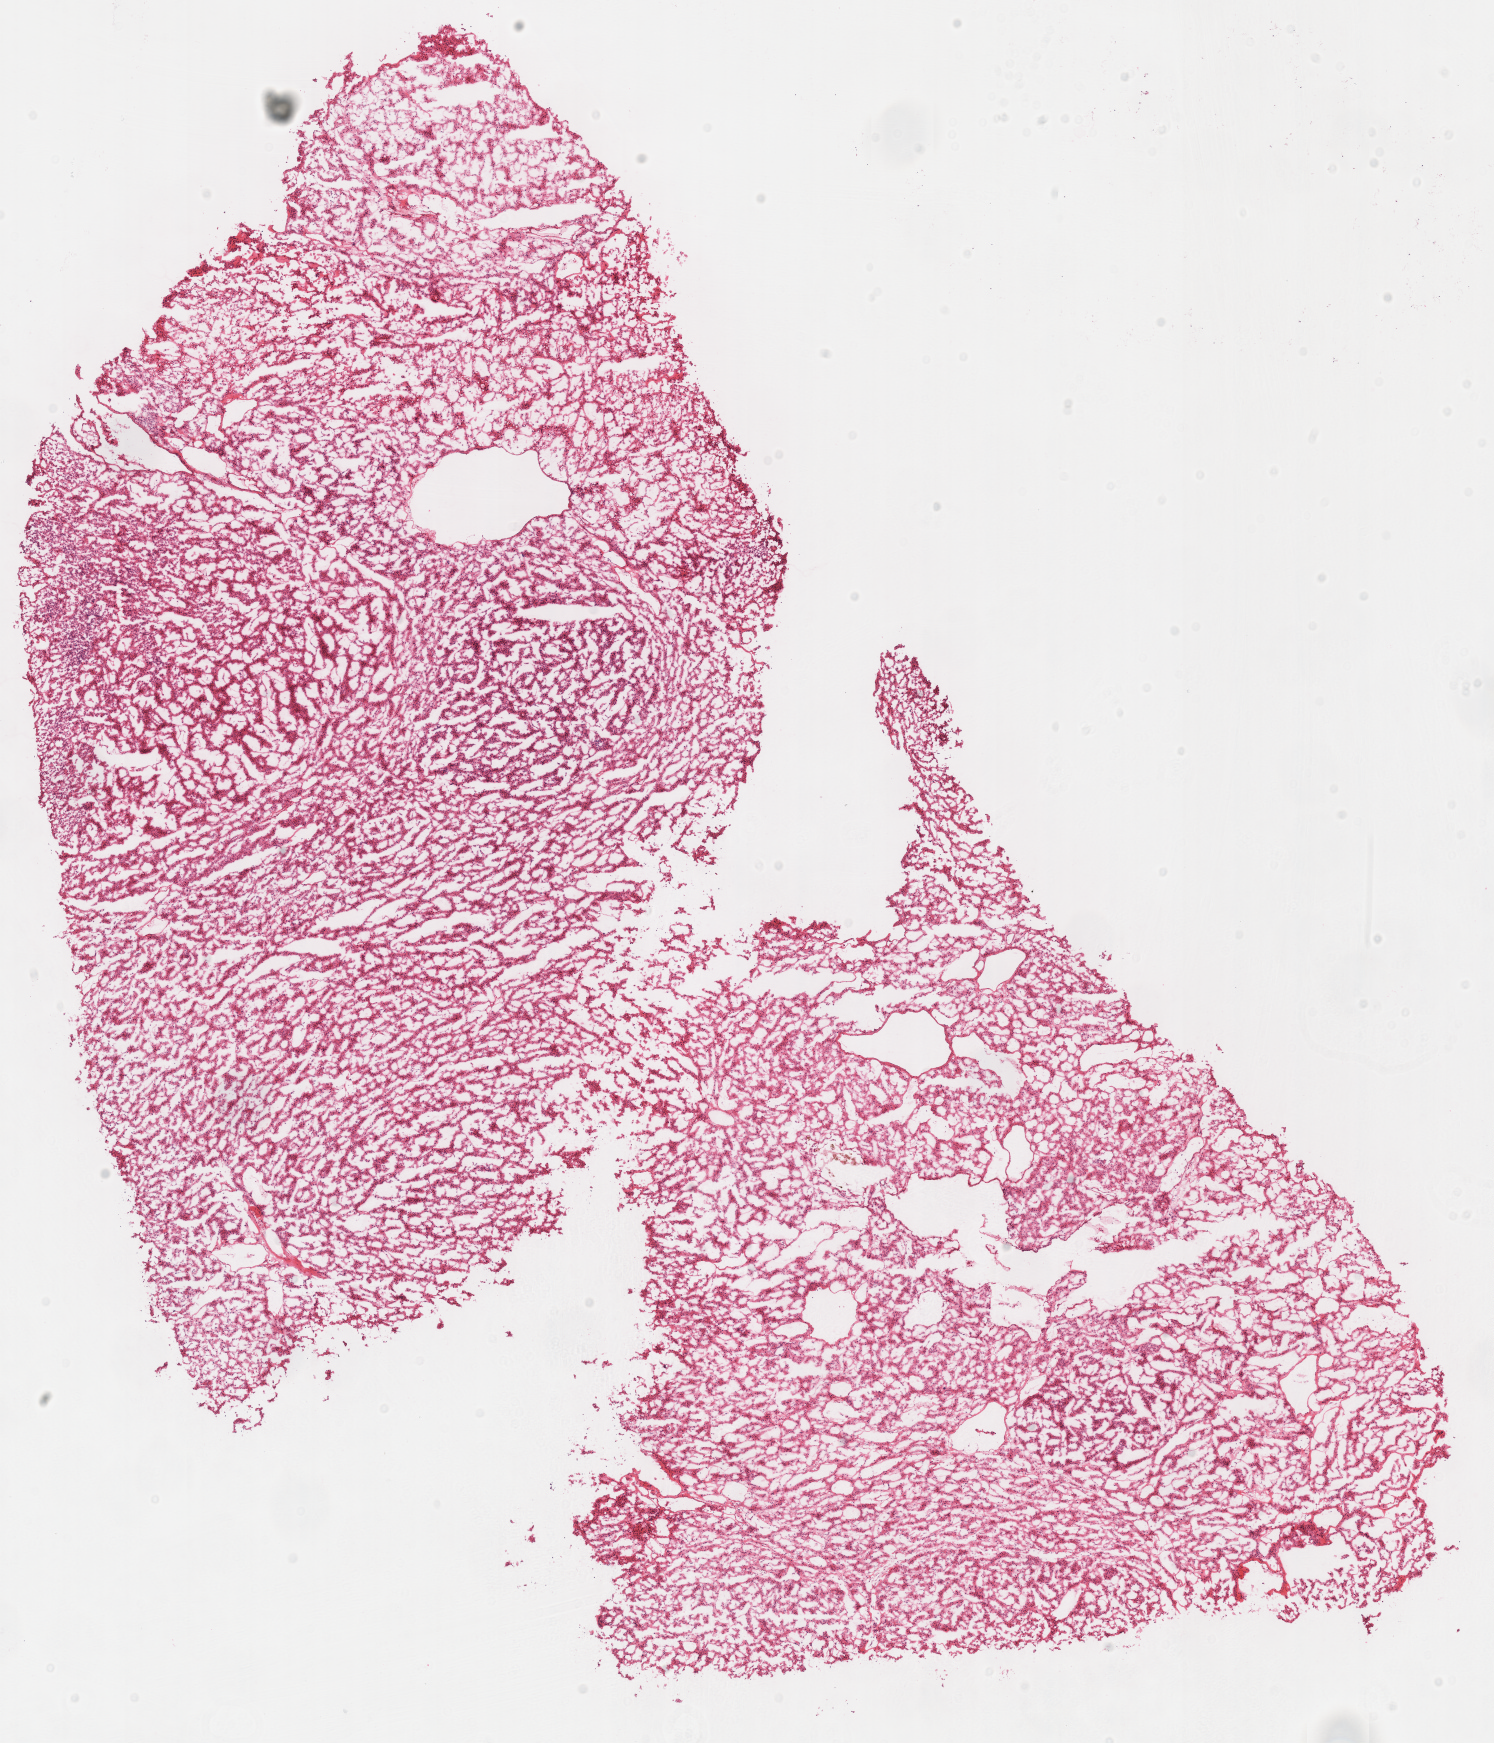
Whole-slide histology image, H&E, whole scanned area (about 11.7 x 13.7 mm, slide scanned at 40x) shown as a low-resolution overview. Frozen section from the top of the tissue portion. Primary tumour sample from the kidney. Female patient; age at initial diagnosis 86 years. Slide review estimates, as recorded: tumour cells 100%, tumour nuclei 95%, normal cells 0%, stromal cells 0%, necrosis 0%. Infiltration values recorded for this section: lymphocyte infiltration 0%, monocyte infiltration 0%, neutrophil infiltration 0%.
Diagnosis: Renal cell carcinoma, chromophobe type. AJCC pathologic stage: II (7th edition).